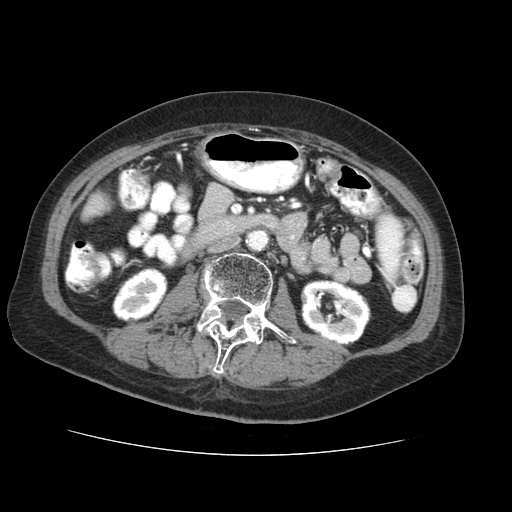
Contrast-enhanced abdominal CT (liver protocol), one axial slice; position 3 of 73 along the scan axis; reconstruction kernel STANDARD; 120 kVp; soft-tissue window (W 400 / L 40 HU); 2.5 mm slice thickness; 512 × 512 image matrix, field of view 360 × 360 mm. Case-level facts recorded for this patient, not image findings: diagnosis: hepatocellular carcinoma (patient treated with transarterial chemoembolisation; whether this scan precedes or follows treatment is not stated here); TNM stage (as recorded): Stage-IVB; Child-Pugh class: A; tumour nodularity: uninodular.
Annotated regions visible in this slice (semi-automatic segmentation, software-assisted and operator-edited):
- liver parenchyma outside the tumour (the mass and vessels are separate outlines, so this box may not span the whole liver): box from (x=82, y=194) to (x=106, y=220) px